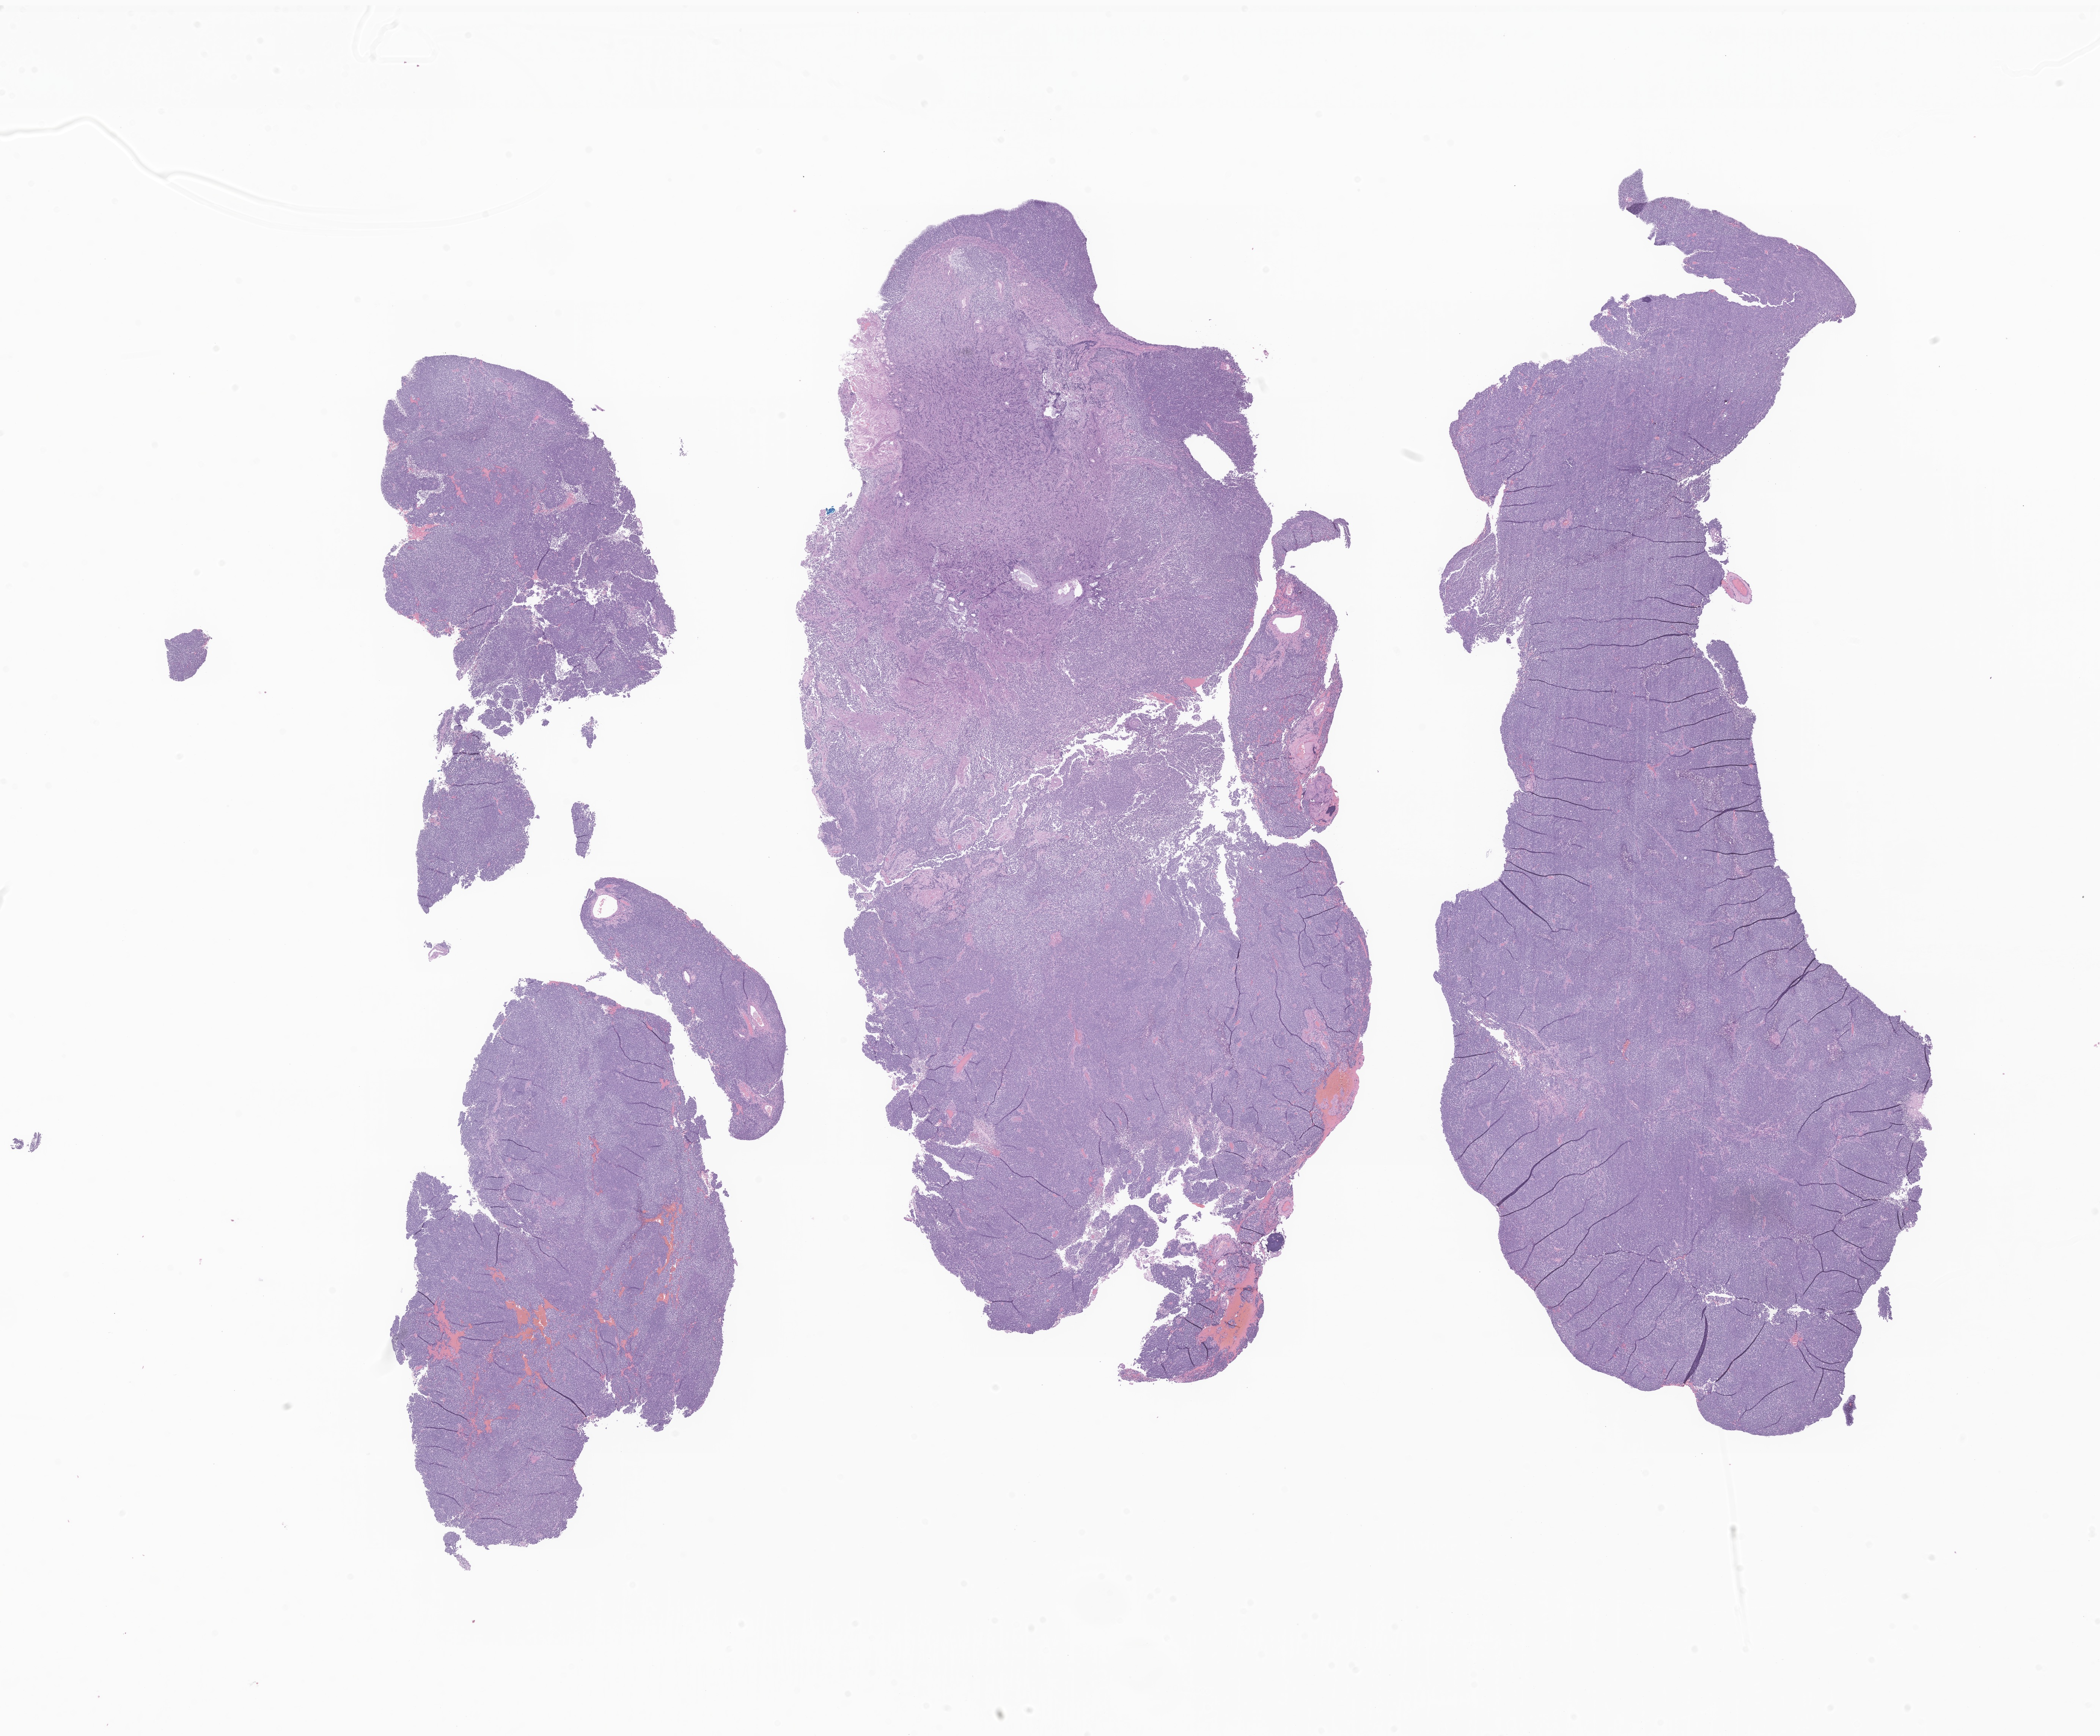
Whole-slide image, hematoxylin and eosin (H&E) stain of tumor tissue from the brain, low-resolution overview of the scanned area, about 23.3 x 19.3 mm. FFPE section. Patient: male, age 51 months (4 years 3 months).
* recorded diagnosis: Medulloblastoma, NOS